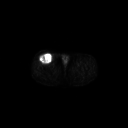
FDG PET of an extremity soft-tissue mass (from a PET/CT study), one axial slice; position 274 of 311 along the scan axis; 3.27 mm slice thickness; 128 × 128 image matrix. Male patient, age 56 years. Case-level facts recorded for this patient, not image findings: histological type: pleiomorphic leiomyosarcoma; grade: intermediate; site of the primary tumour: right thigh.
Outlined on this slice (expert contour drawn on MRI and transferred to this co-registered scan by the dataset authors):
- gross tumour volume including surrounding oedema: bounding box [x1, y1, x2, y2] px = [39, 53, 53, 64]
- gross tumour volume (mass): [39, 53, 53, 64]